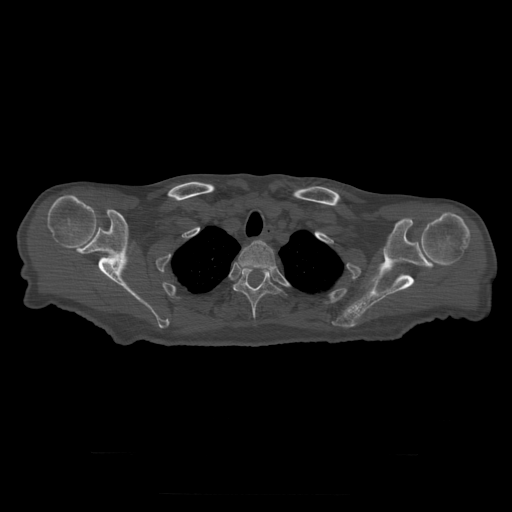
CT including the spine, one axial slice; slice 262 of 397 in the series (ordered by position); 120 kVp; bone window (W 1800 / L 400 HU); 512 × 512 image matrix, field of view 510 × 510 mm. Patient age 73 years. Case-level facts recorded for this patient, not image findings: primary cancer: prostate.
Structures marked on this image (semi-automatic segmentation, software-assisted and operator-edited):
- T2 vertebra: bounding box <238,240,276,271> (left, top, right, bottom; pixels)
- T3 vertebra: <234,268,282,322>
- T4 vertebra: <226,305,228,307>